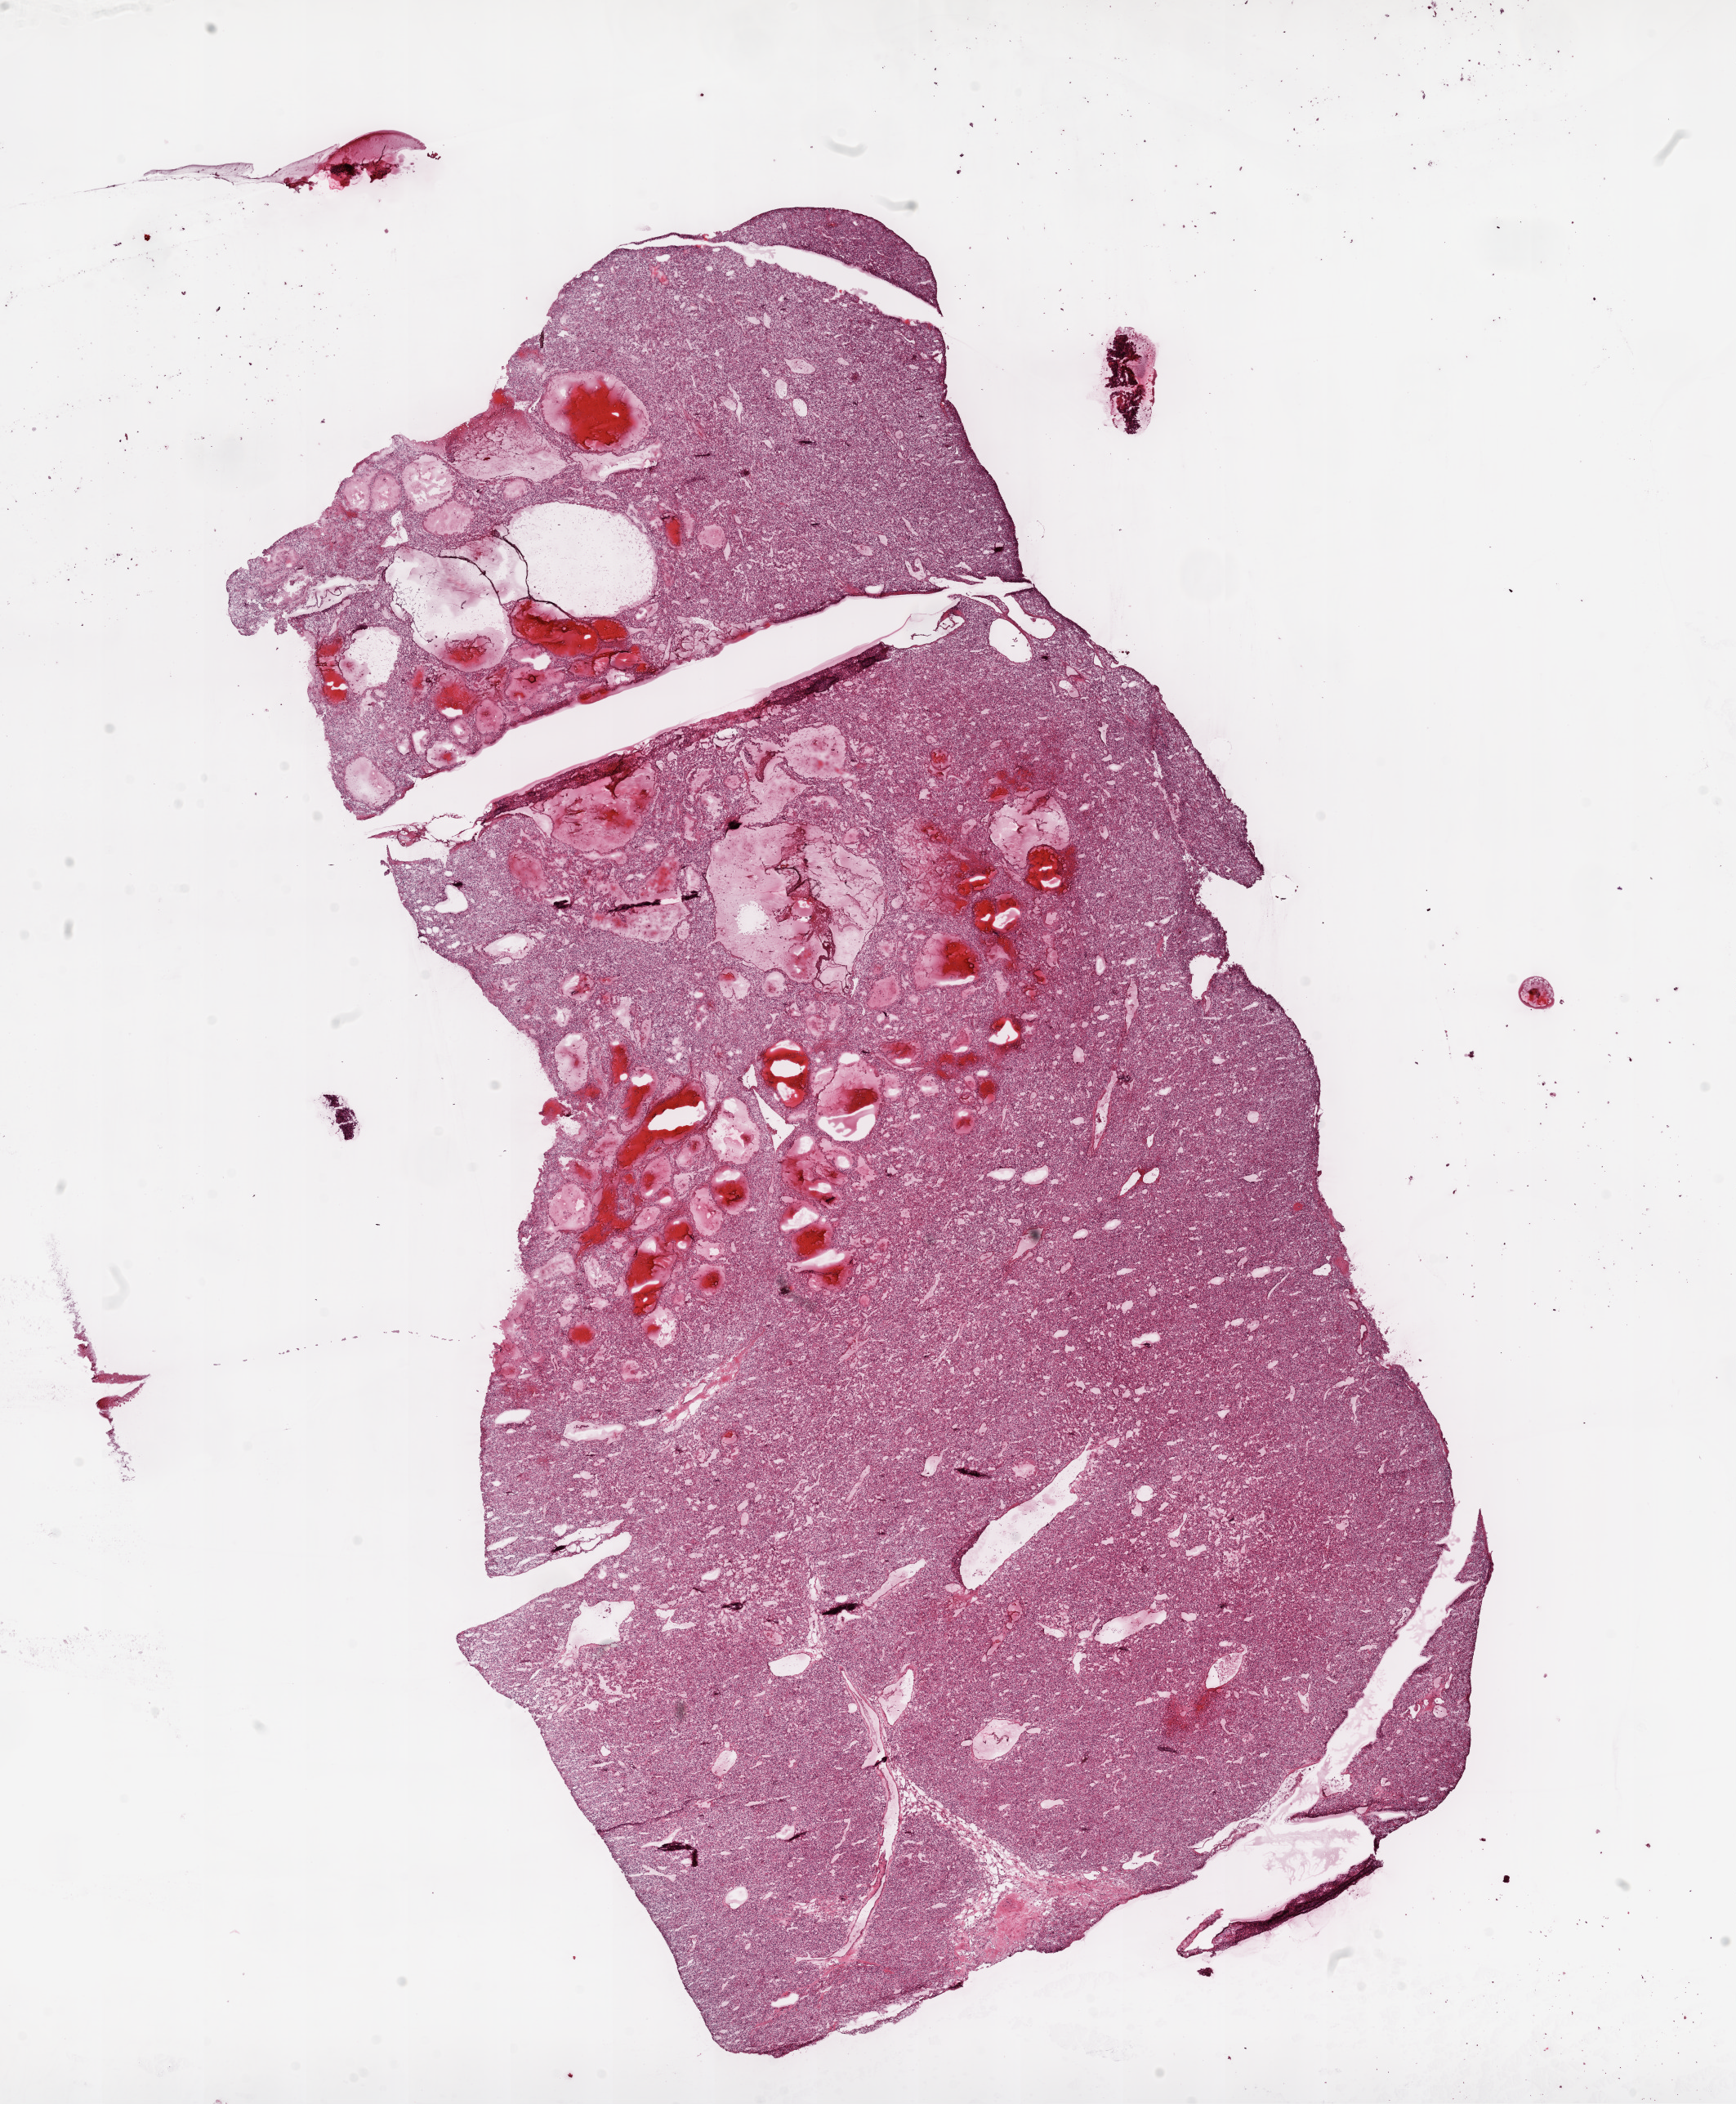
Digitized Hematoxylin and eosin (H&E) stained tissue section (whole slide), a low-resolution overview of the entire scanned area, about 17.1 x 20.7 mm. Frozen section from the top of the tissue portion. Kidney, primary tumour sample. Patient: male, age at initial diagnosis 67 years. Histologic grade: G2 (moderately differentiated). Composition of this section per pathologist review: tumour cells 95%, tumour nuclei 85%, normal cells 0%, stromal cells 5%, necrosis 0%.
- diagnosis: Clear cell adenocarcinoma, NOS
- laterality: left
- AJCC pathologic stage: III